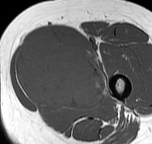
MRI of an extremity soft-tissue mass, one axial slice; position 26 of 57 along the scan axis; MR volume resampled by the dataset authors to the PET/CT grid (not the native acquisition matrix); 152 × 144 image matrix, field of view 148 × 141 mm. Female patient. From the clinical record (not read from this slice): histological type: pleiomorphic leiomyosarcoma; grade: intermediate; site of the primary tumour: left thigh.
Outlined on this slice (expert contour drawn on MRI and transferred to this co-registered scan by the dataset authors):
- gross tumour volume including surrounding oedema: bounding box <15,37,108,109> (left, top, right, bottom; pixels)
- gross tumour volume (mass): <15,37,106,107>